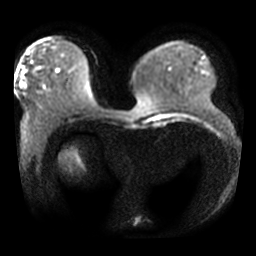
Breast MRI, one axial slice. Position 12 of 42 along the scan axis. Diffusion-weighted series; image 2 of 4 stored at this slice position (different b-values; order by instance number). 3 T. 5 mm slice thickness. 256 × 256 image matrix, field of view 360 × 360 mm. Female patient.
Structures marked on this image (expert manual segmentation):
- tumour on diffusion-weighted imaging: box from (x=24, y=82) to (x=26, y=87) px